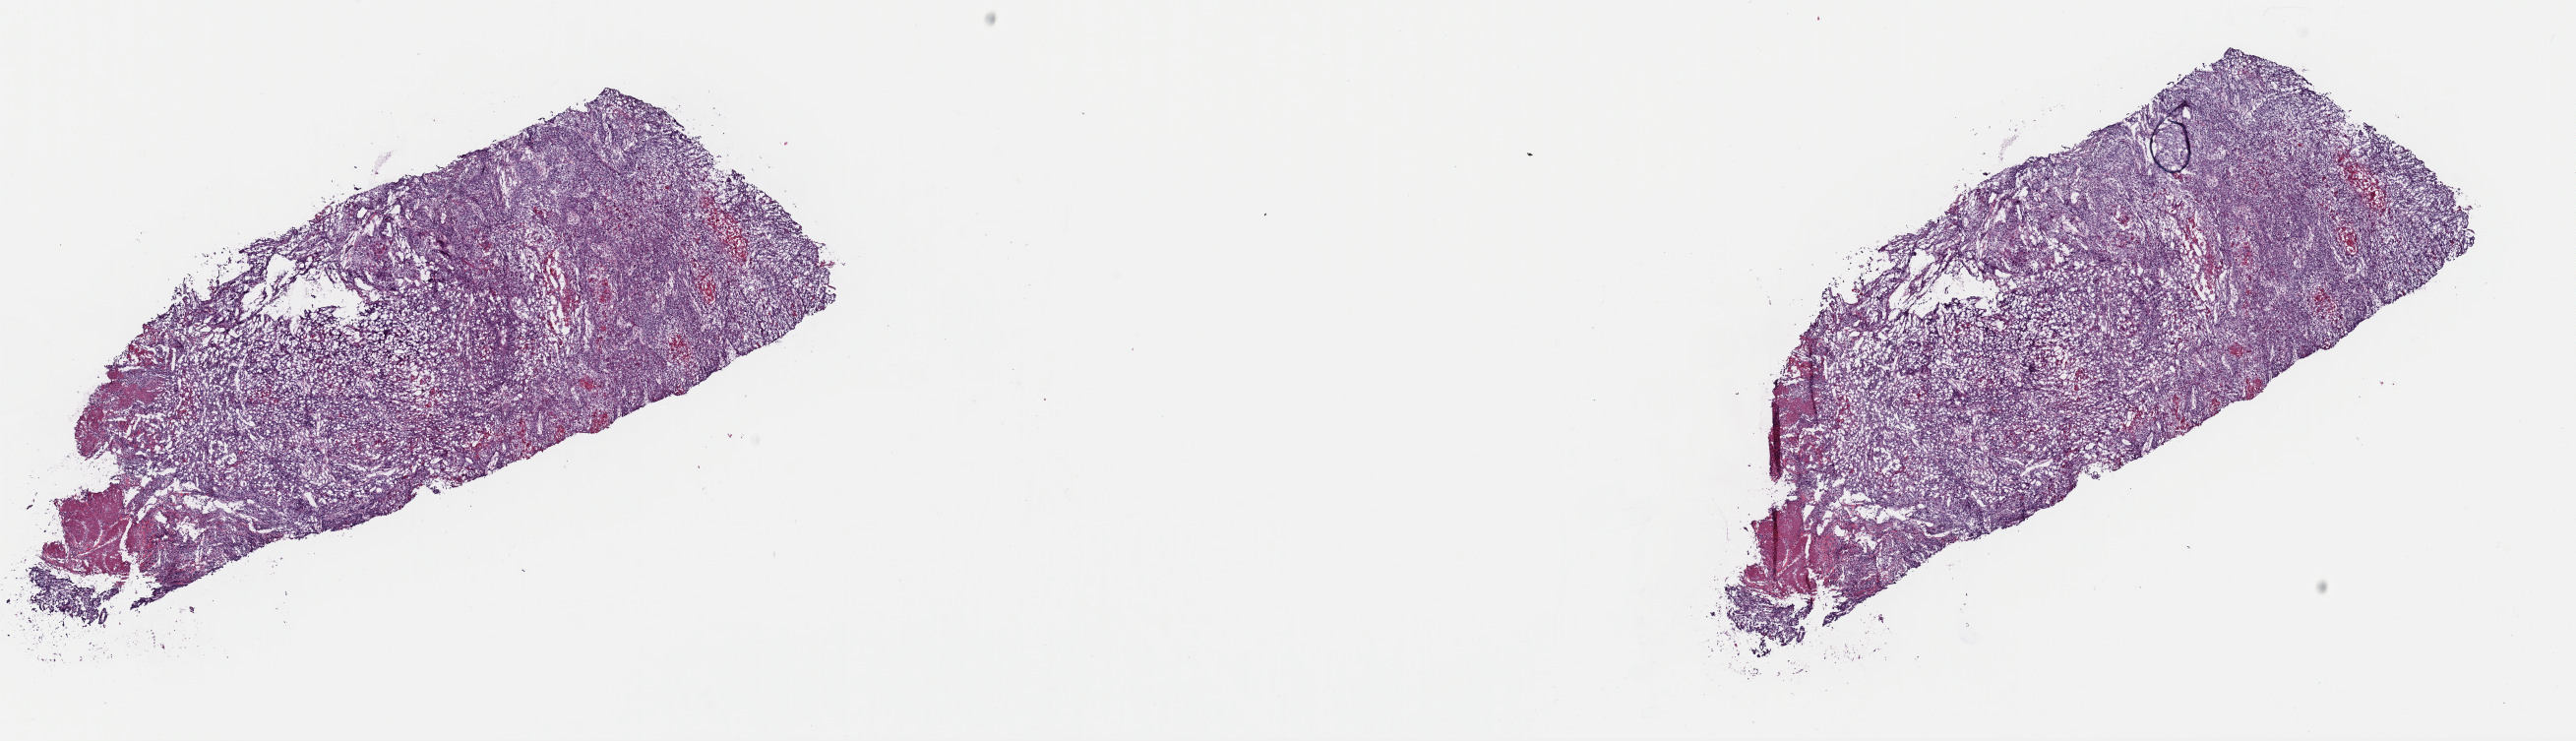
Whole-slide histology image, Hematoxylin and eosin (H&E) stained — shown as a low-resolution overview of the whole scanned area (about 20.7 x 5.9 mm, slide scanned at 40x); frozen section; primary tumour sample from the bladder. Male, age 83 years at initial diagnosis. Histologic grade: high grade. Slide review estimates, as recorded: tumour cells 82%, tumour nuclei 85%, normal cells 0%, stromal cells 15%, necrosis 3%. Infiltration values recorded for this section: lymphocyte infiltration 3%, monocyte infiltration 2%, neutrophil infiltration 0%.
• lymph nodes positive (case pathology): 0 of 5 examined
• TNM: T2b N0 MX
• pathologic diagnosis: Transitional cell carcinoma
• AJCC pathologic stage: II (7th edition)